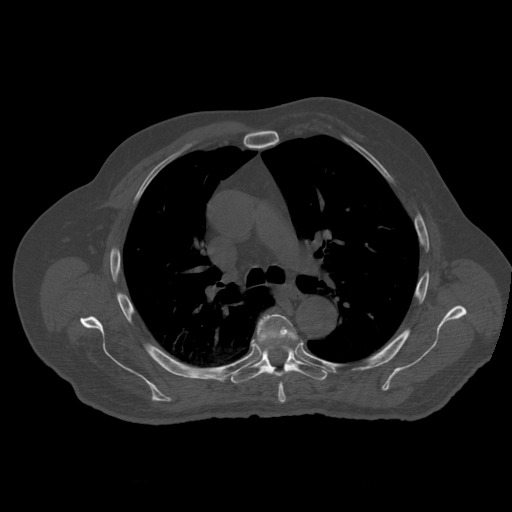
CT including the spine, one axial slice; position 390 of 399 along the scan axis; 120 kVp; bone window (W 1800 / L 400 HU); 1.25 mm slice thickness; 512 × 512 image matrix. Patient age 73 years. From the clinical record (not read from this slice): primary cancer: prostate.
Structures marked on this image (semi-automatically segmented with operator editing):
- T5 vertebra: box from (x=257, y=314) to (x=298, y=403) px
- T6 vertebra: (x=231, y=341)–(x=327, y=384)